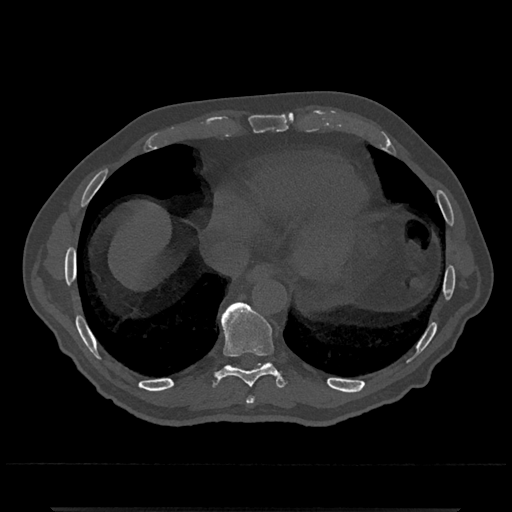
CT including the spine, one axial slice. Slice 607 of 797 in the series (ordered by position). 120 kVp. Bone window (W 1800 / L 400 HU). 0.5 mm slice thickness. 512 × 512 image matrix, field of view 393 × 393 mm. Male patient, age 67 years. From the clinical record (not read from this slice): primary cancer: prostate.
Outlined on this slice (semi-automatic segmentation, software-assisted and operator-edited):
- T8 vertebra: bounding box (x1, y1, x2, y2) in pixels: (247, 396, 255, 404)
- T9 vertebra: (216, 301, 284, 388)